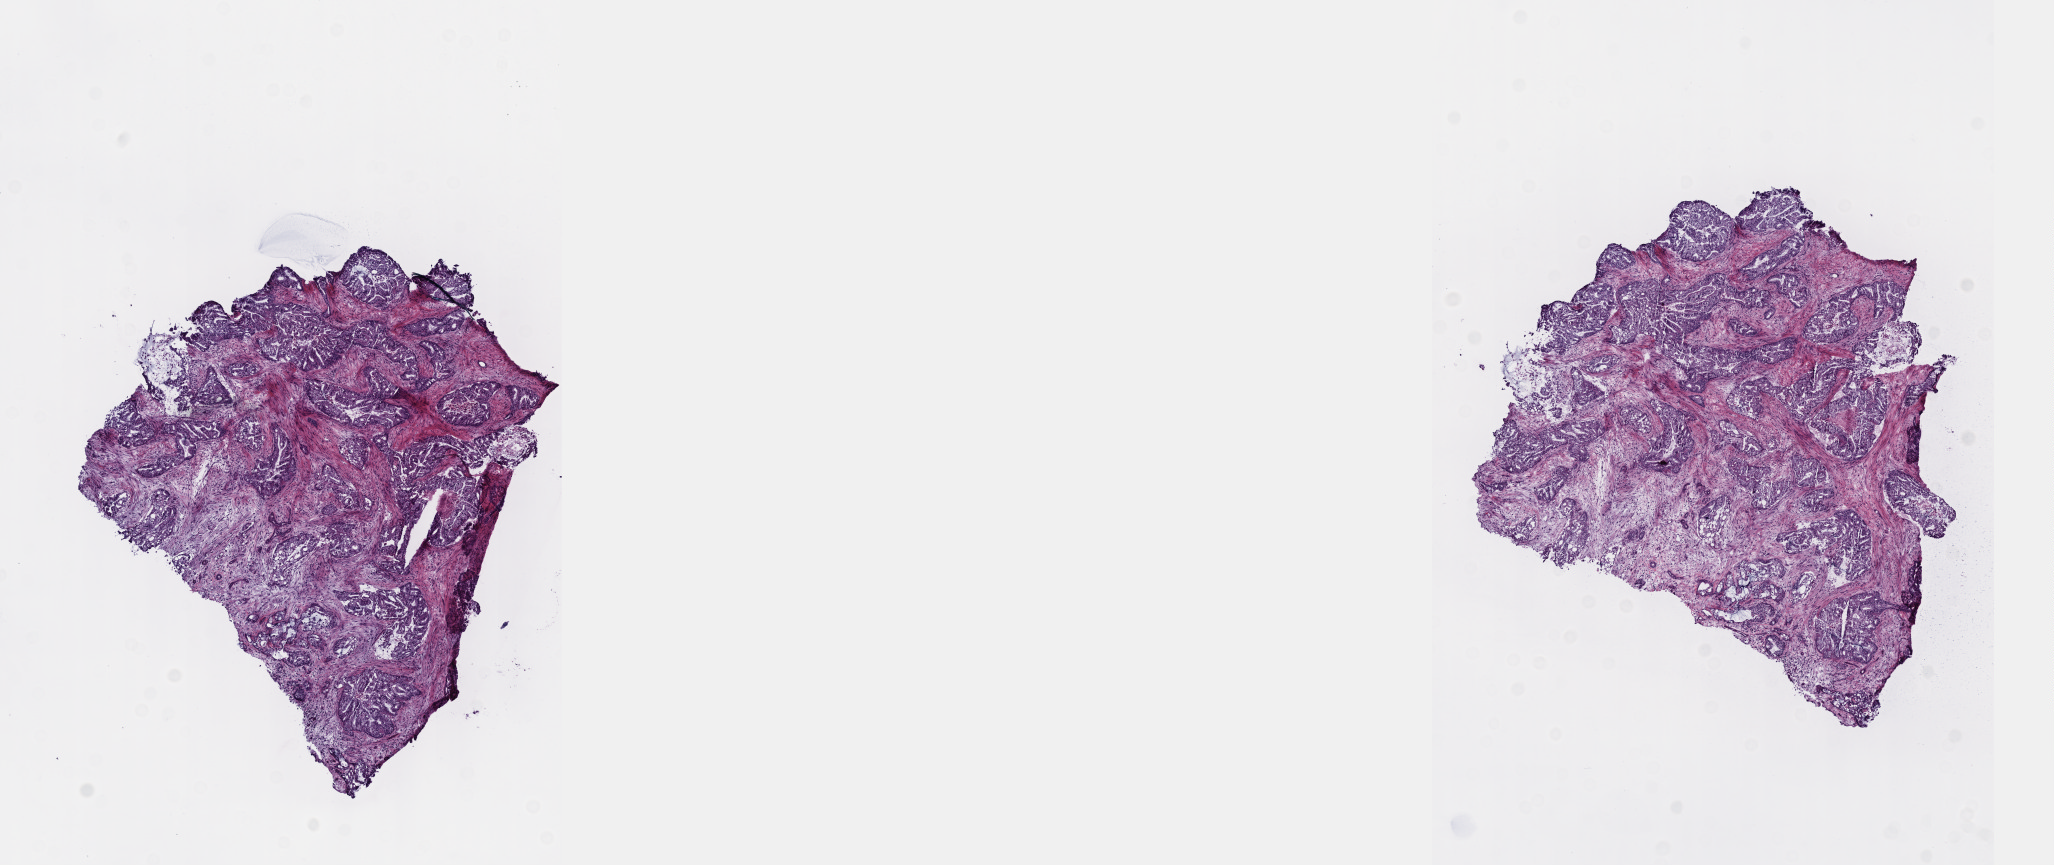
Whole-slide histology image, Hematoxylin and eosin (H&E) stained — low-resolution overview of the scanned area, about 16.6 x 7.0 mm; frozen section; sample: primary tumour, pancreas. Male patient; age at initial diagnosis 76 years. Histologic grade: G2 (moderately differentiated). Composition of this section per pathologist review: tumour cells 60%, tumour nuclei 60%, normal cells 0%, stromal cells 30%, necrosis 10%. Infiltration values recorded for this section: lymphocyte infiltration 40%, monocyte infiltration 20%, neutrophil infiltration 20%.
Diagnosis: Infiltrating duct carcinoma, NOS (head of pancreas). AJCC pathologic stage: IIA.